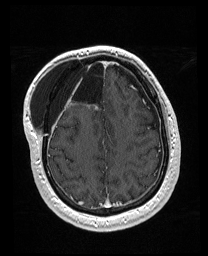
Brain MRI from a brain-tumour surgery series, one axial slice. Position 55 of 176 along the scan axis. T1-weighted post-contrast. 1 mm slice thickness. 208 × 256 image matrix, field of view 208 × 256 mm. From the clinical record (not read from this slice): histopathology: Astrocytoma; WHO grade: 4.
Outlined on this slice (manually delineated by an expert):
- previous resection cavity: box from (x=69, y=59) to (x=101, y=102) px